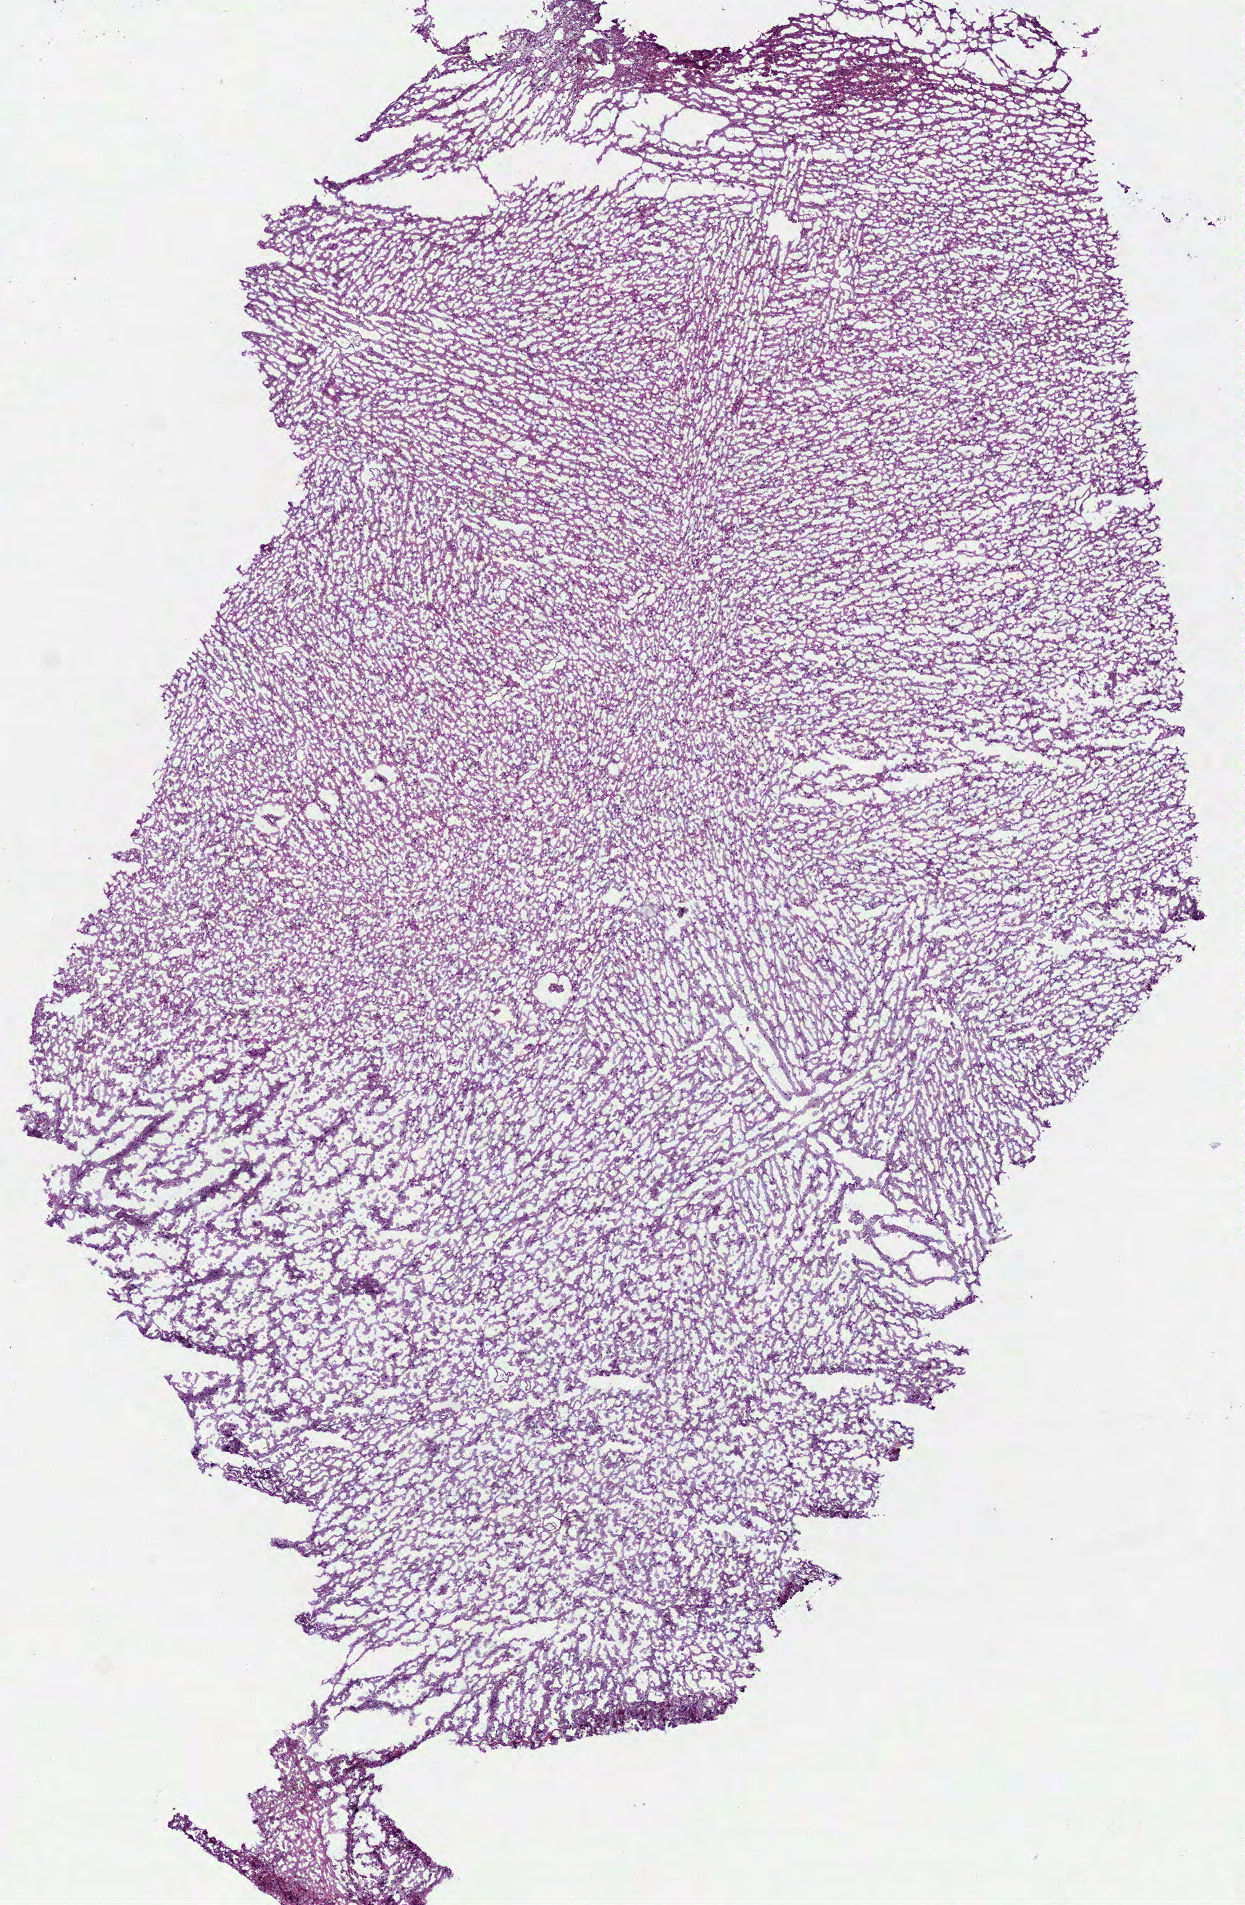
Digitized Hematoxylin and eosin (H&E) stained tissue section (whole slide), shown as a low-resolution overview of the whole scanned area (about 5.0 x 7.7 mm); frozen section from the bottom of the tissue portion; brain, primary tumour sample. Male, age 43 years at initial diagnosis. Histologic grade: G3 (poorly differentiated). Pathologist review of this section (percent, as recorded): tumour cells 100%, tumour nuclei 60%, normal cells 0%, stromal cells 0%, necrosis 0%.
- laterality: right
- diagnosis: Oligodendroglioma, anaplastic